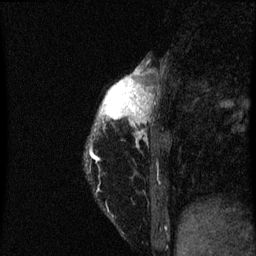
Breast MRI (dynamic contrast-enhanced), one sagittal slice; position 14 of 60 along the scan axis; dynamic contrast-enhanced series, image 2 of 3 at this slice position (ordered by acquisition); 1.5 T; TE 4.2 ms, TR 8 ms; 2 mm slice thickness; 256 × 256 image matrix, field of view 180 × 180 mm. Female patient, age 38 years.
Structures marked on this image (semi-automatically segmented with operator editing):
- analysis volume of interest (the breast-tissue region the enhancement analysis was run in; not a lesion): box from (x=90, y=70) to (x=159, y=151) px
- tumour enhancement mask (voxels above the 70 % enhancement threshold inside the analysis volume of interest): (x=100, y=70)–(x=149, y=123)